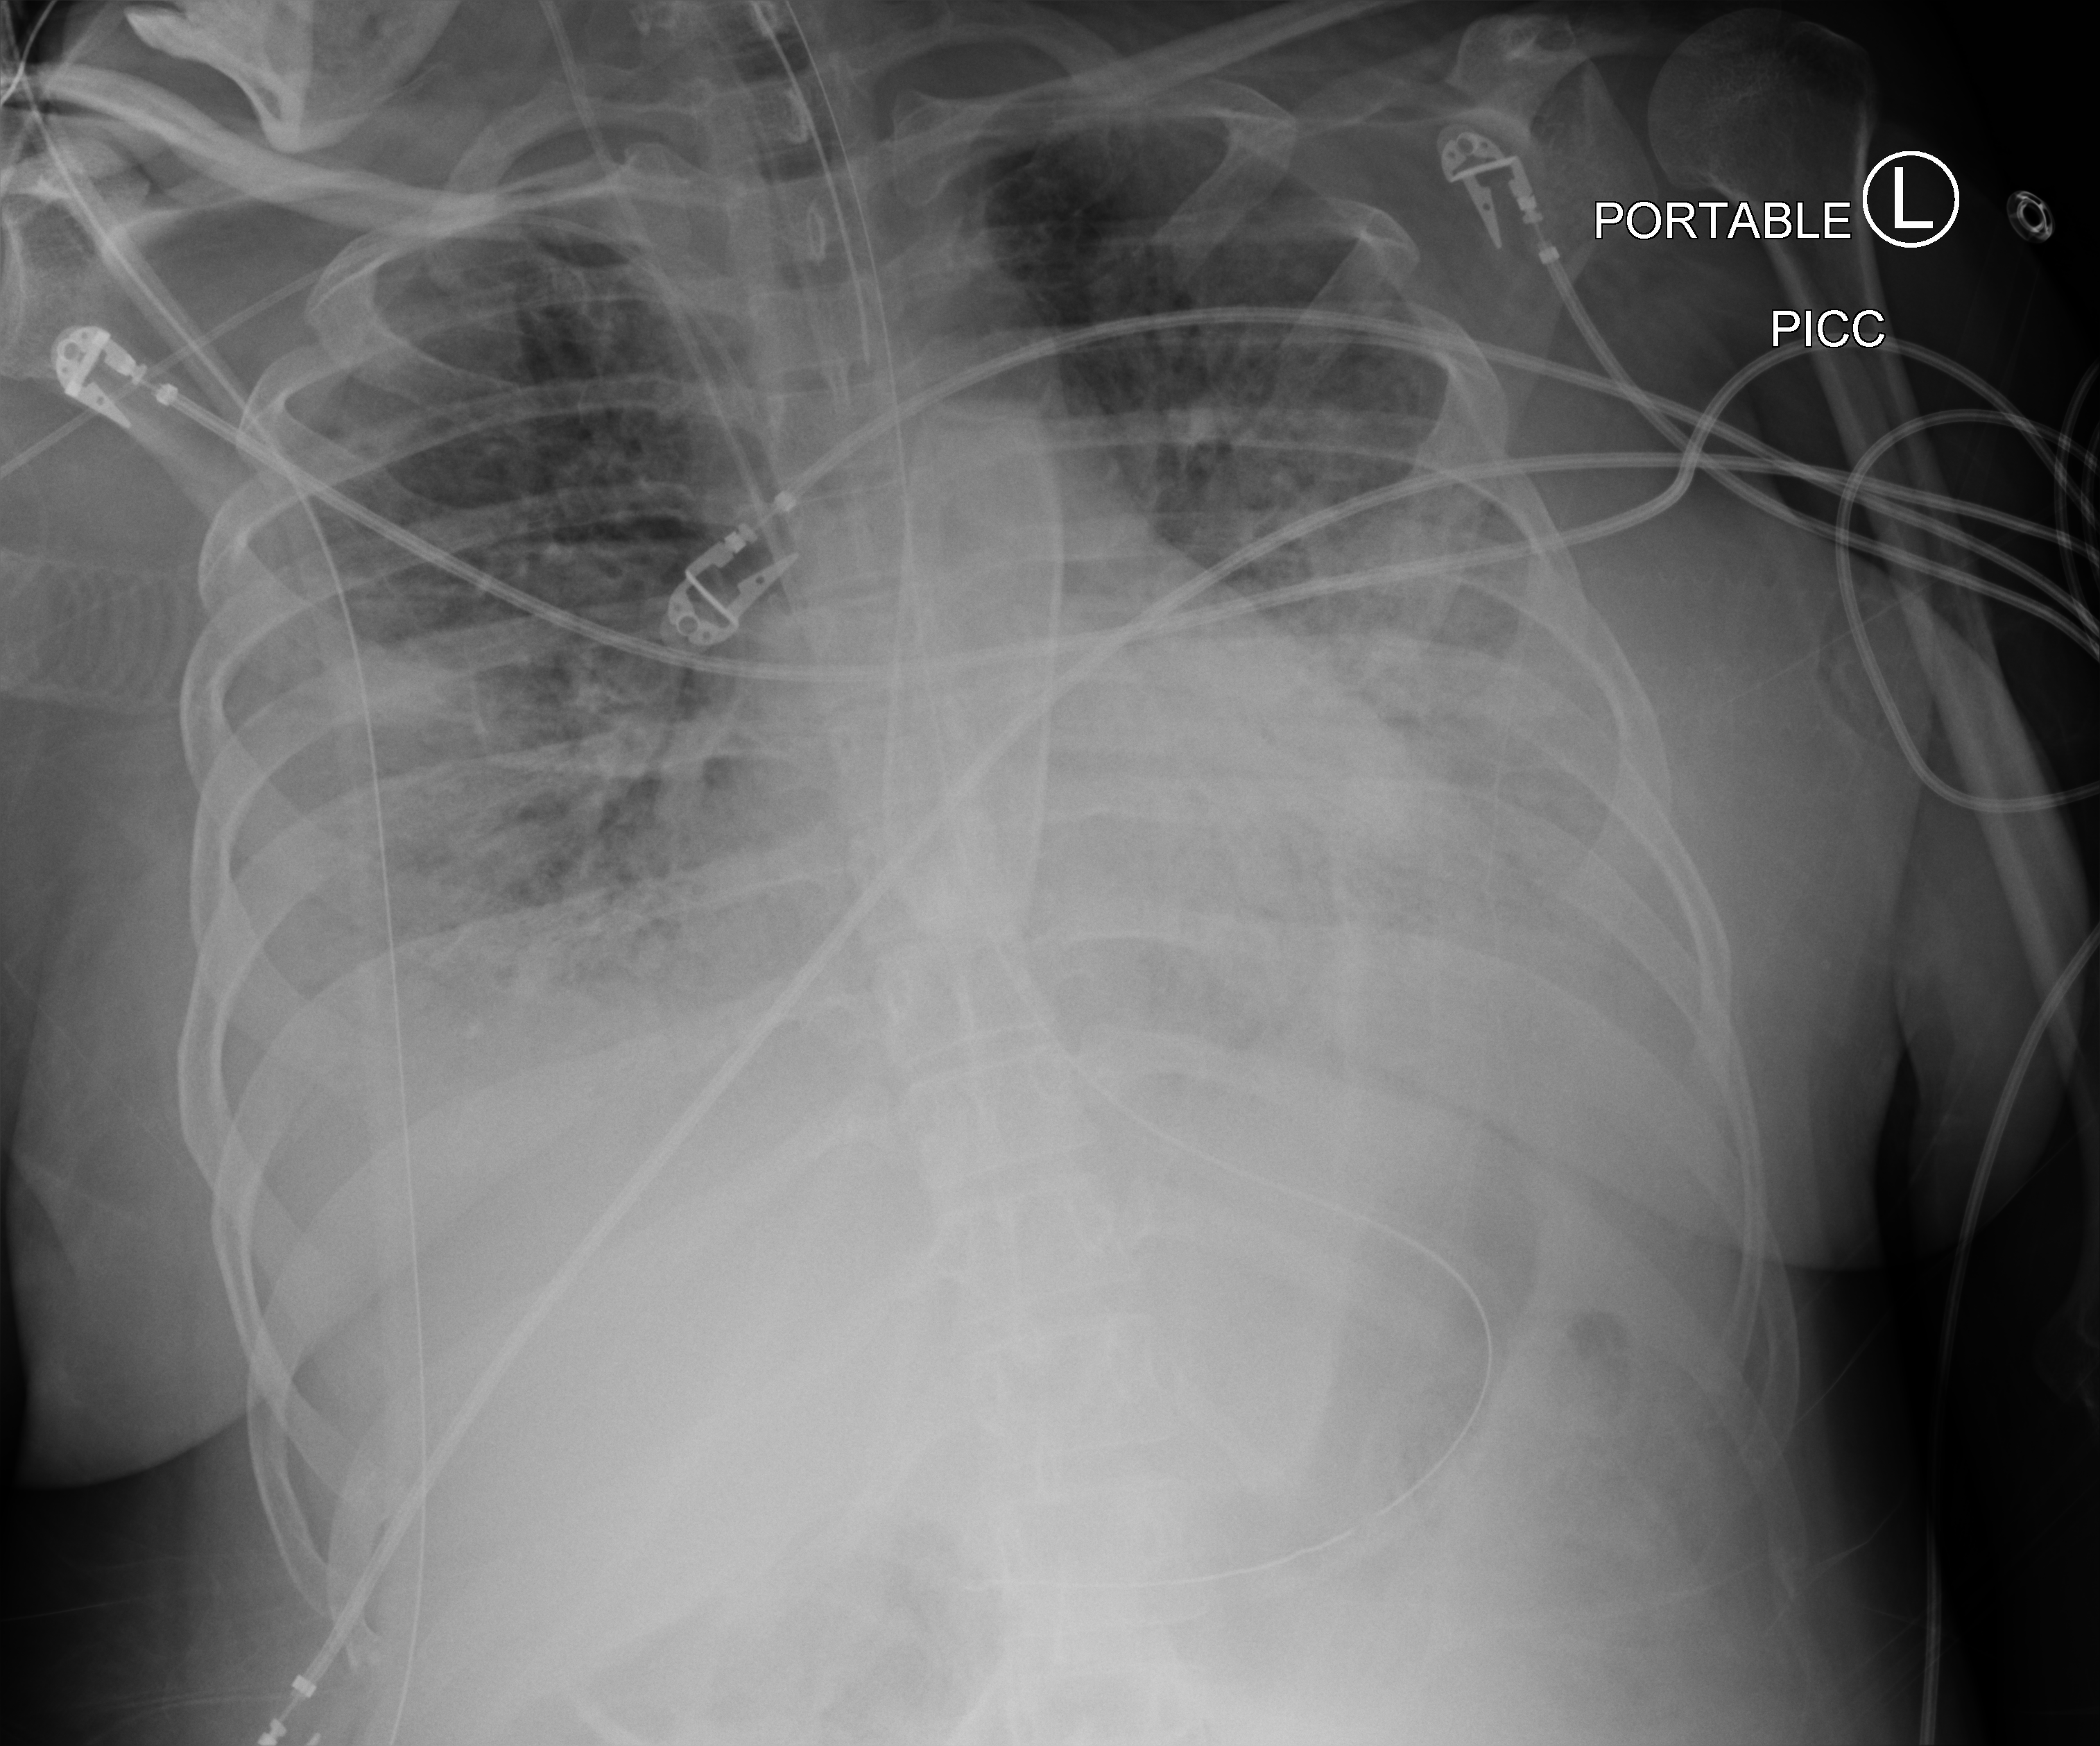
Chest X-ray (portable); anteroposterior (AP) projection. Patient hospitalised with COVID-19, aged 18–59 years.
From the hospital-stay record, not from the radiograph (when in the stay this image was taken is not recorded):
- other chronic lung disease (admission record): no
- admitted to intensive care during this hospital stay: yes
- mechanically ventilated during this hospital stay: yes